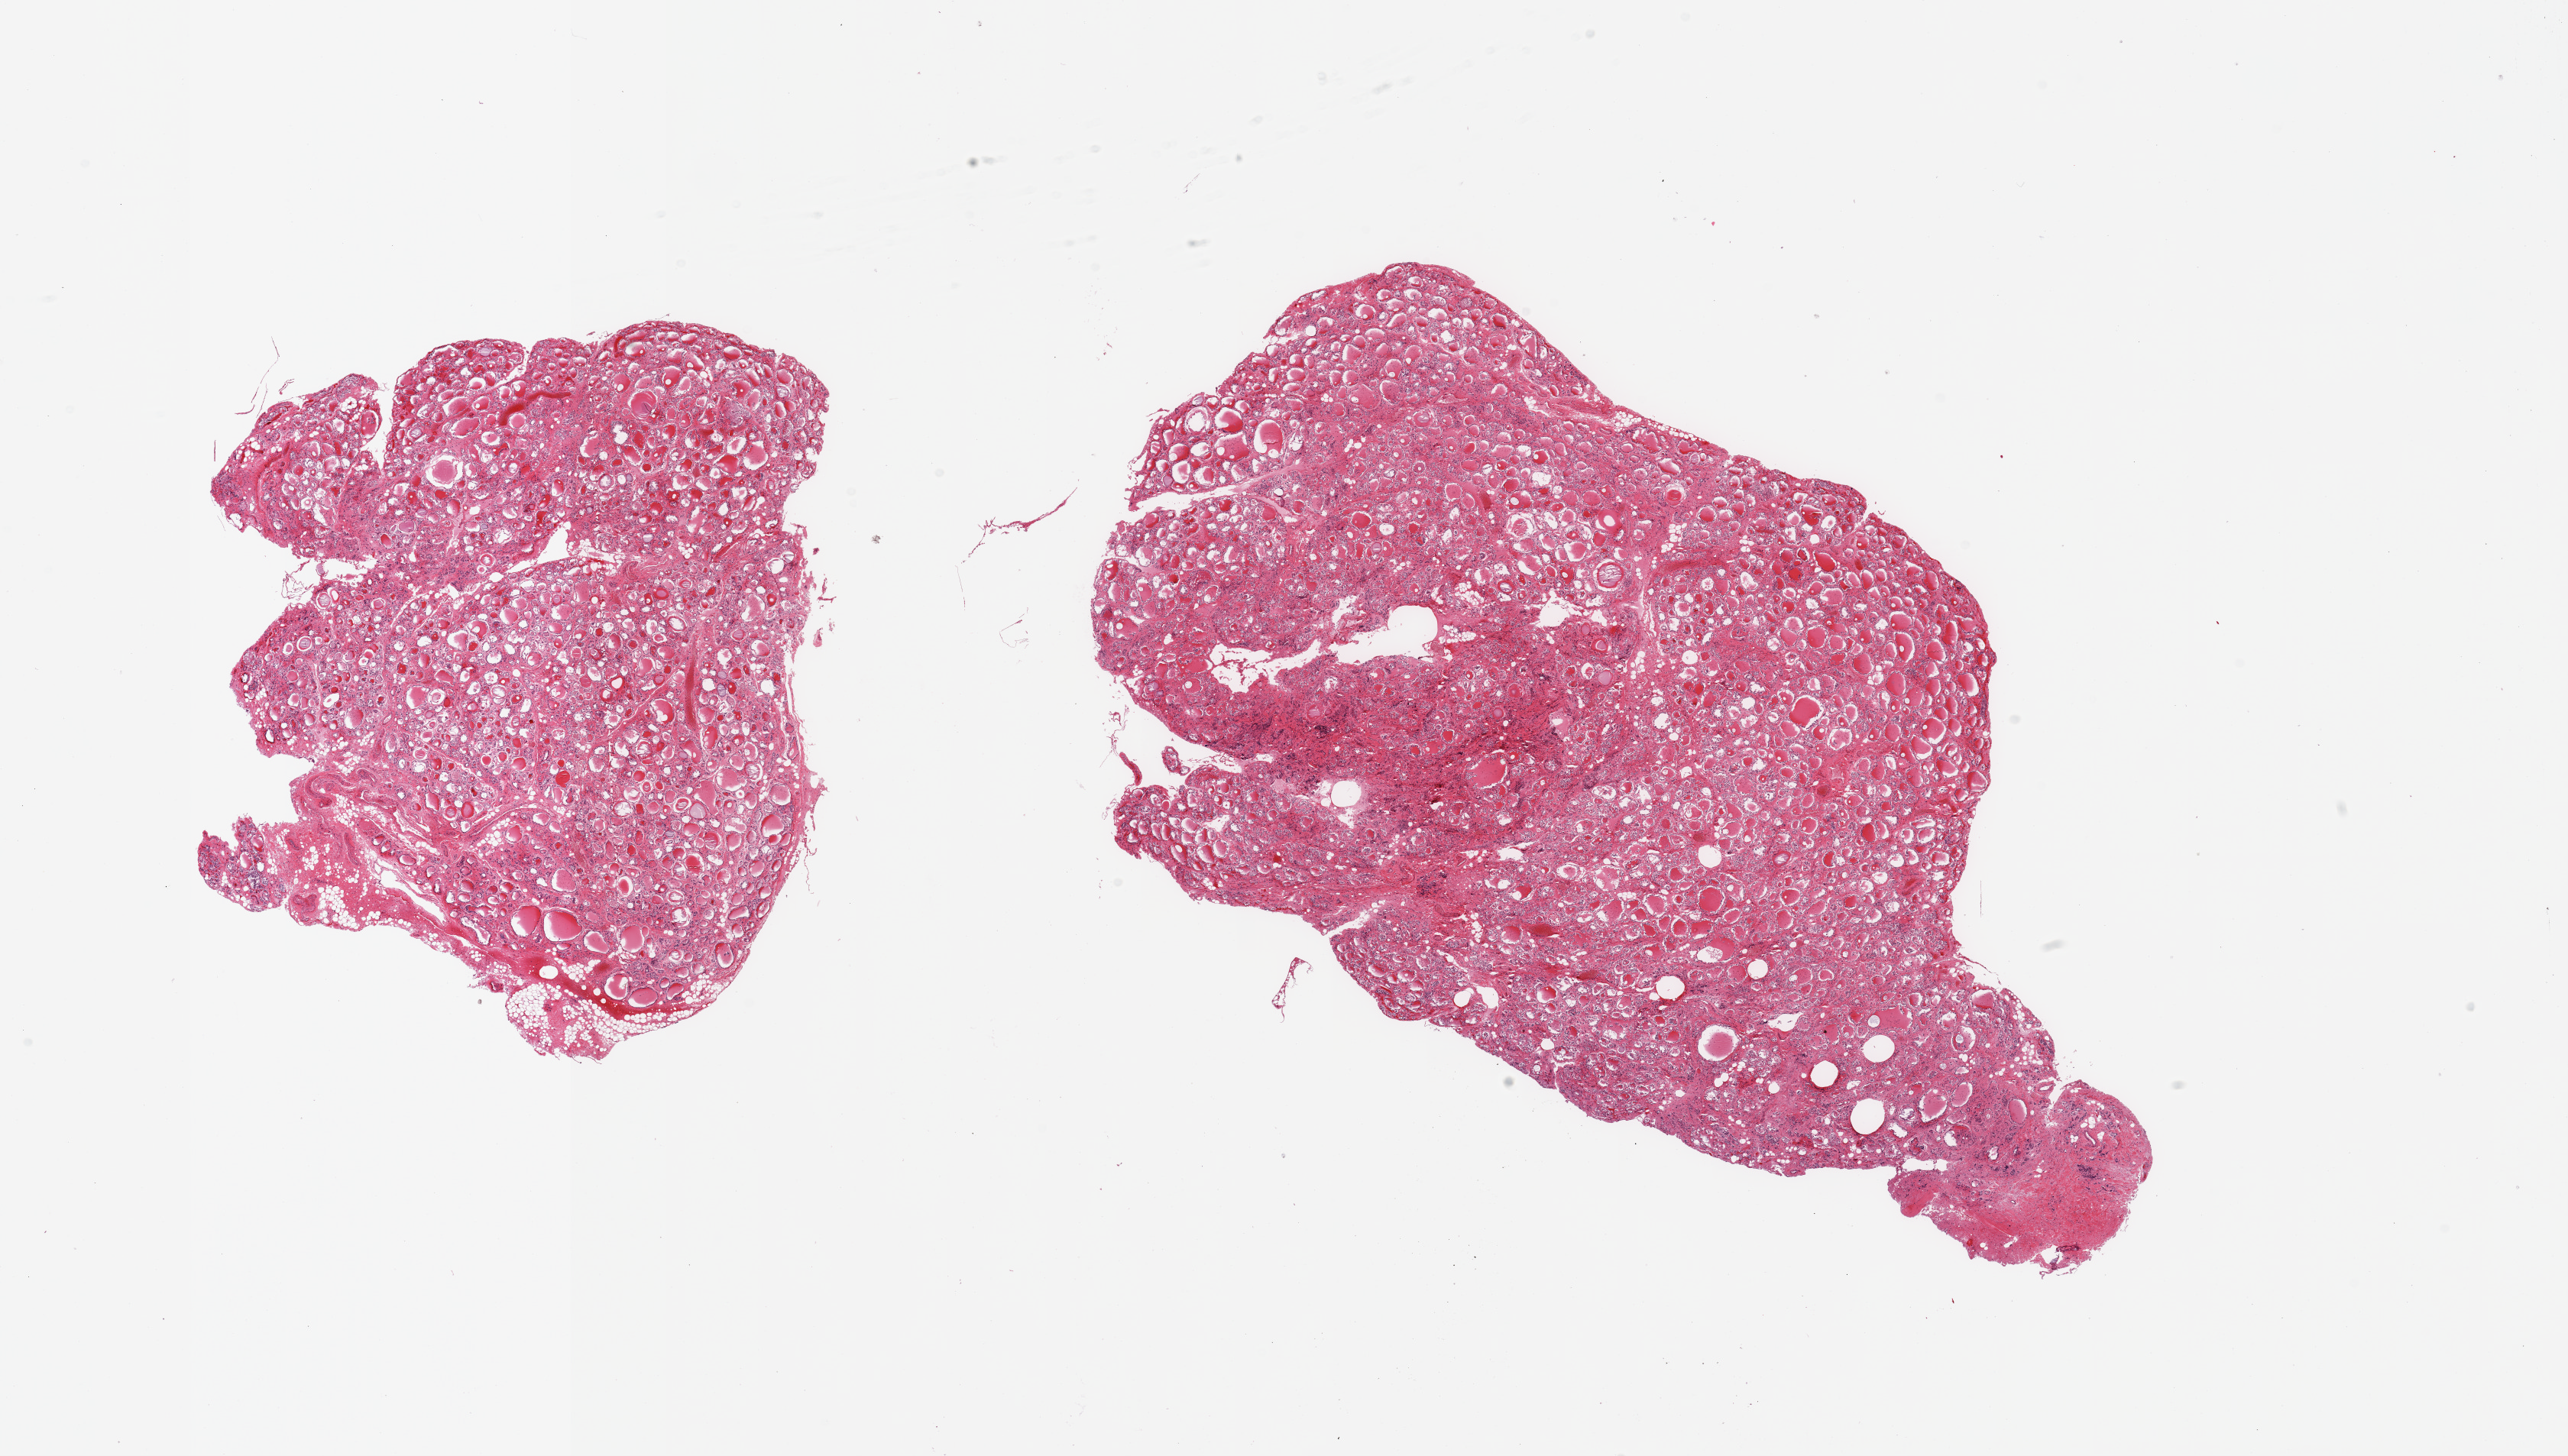
Digitized haematoxylin and eosin-stained section, low-resolution overview of the scanned area, about 26.6 x 15.1 mm (from a 20x scan), PAXgene-fixed paraffin-embedded (PFPE) section, section of thyroid (target tissue), tissue donor sample. Donor: male.
Pathologist's review note for this sample: 2 pieces; minimal attached fat/fibrous tissue.